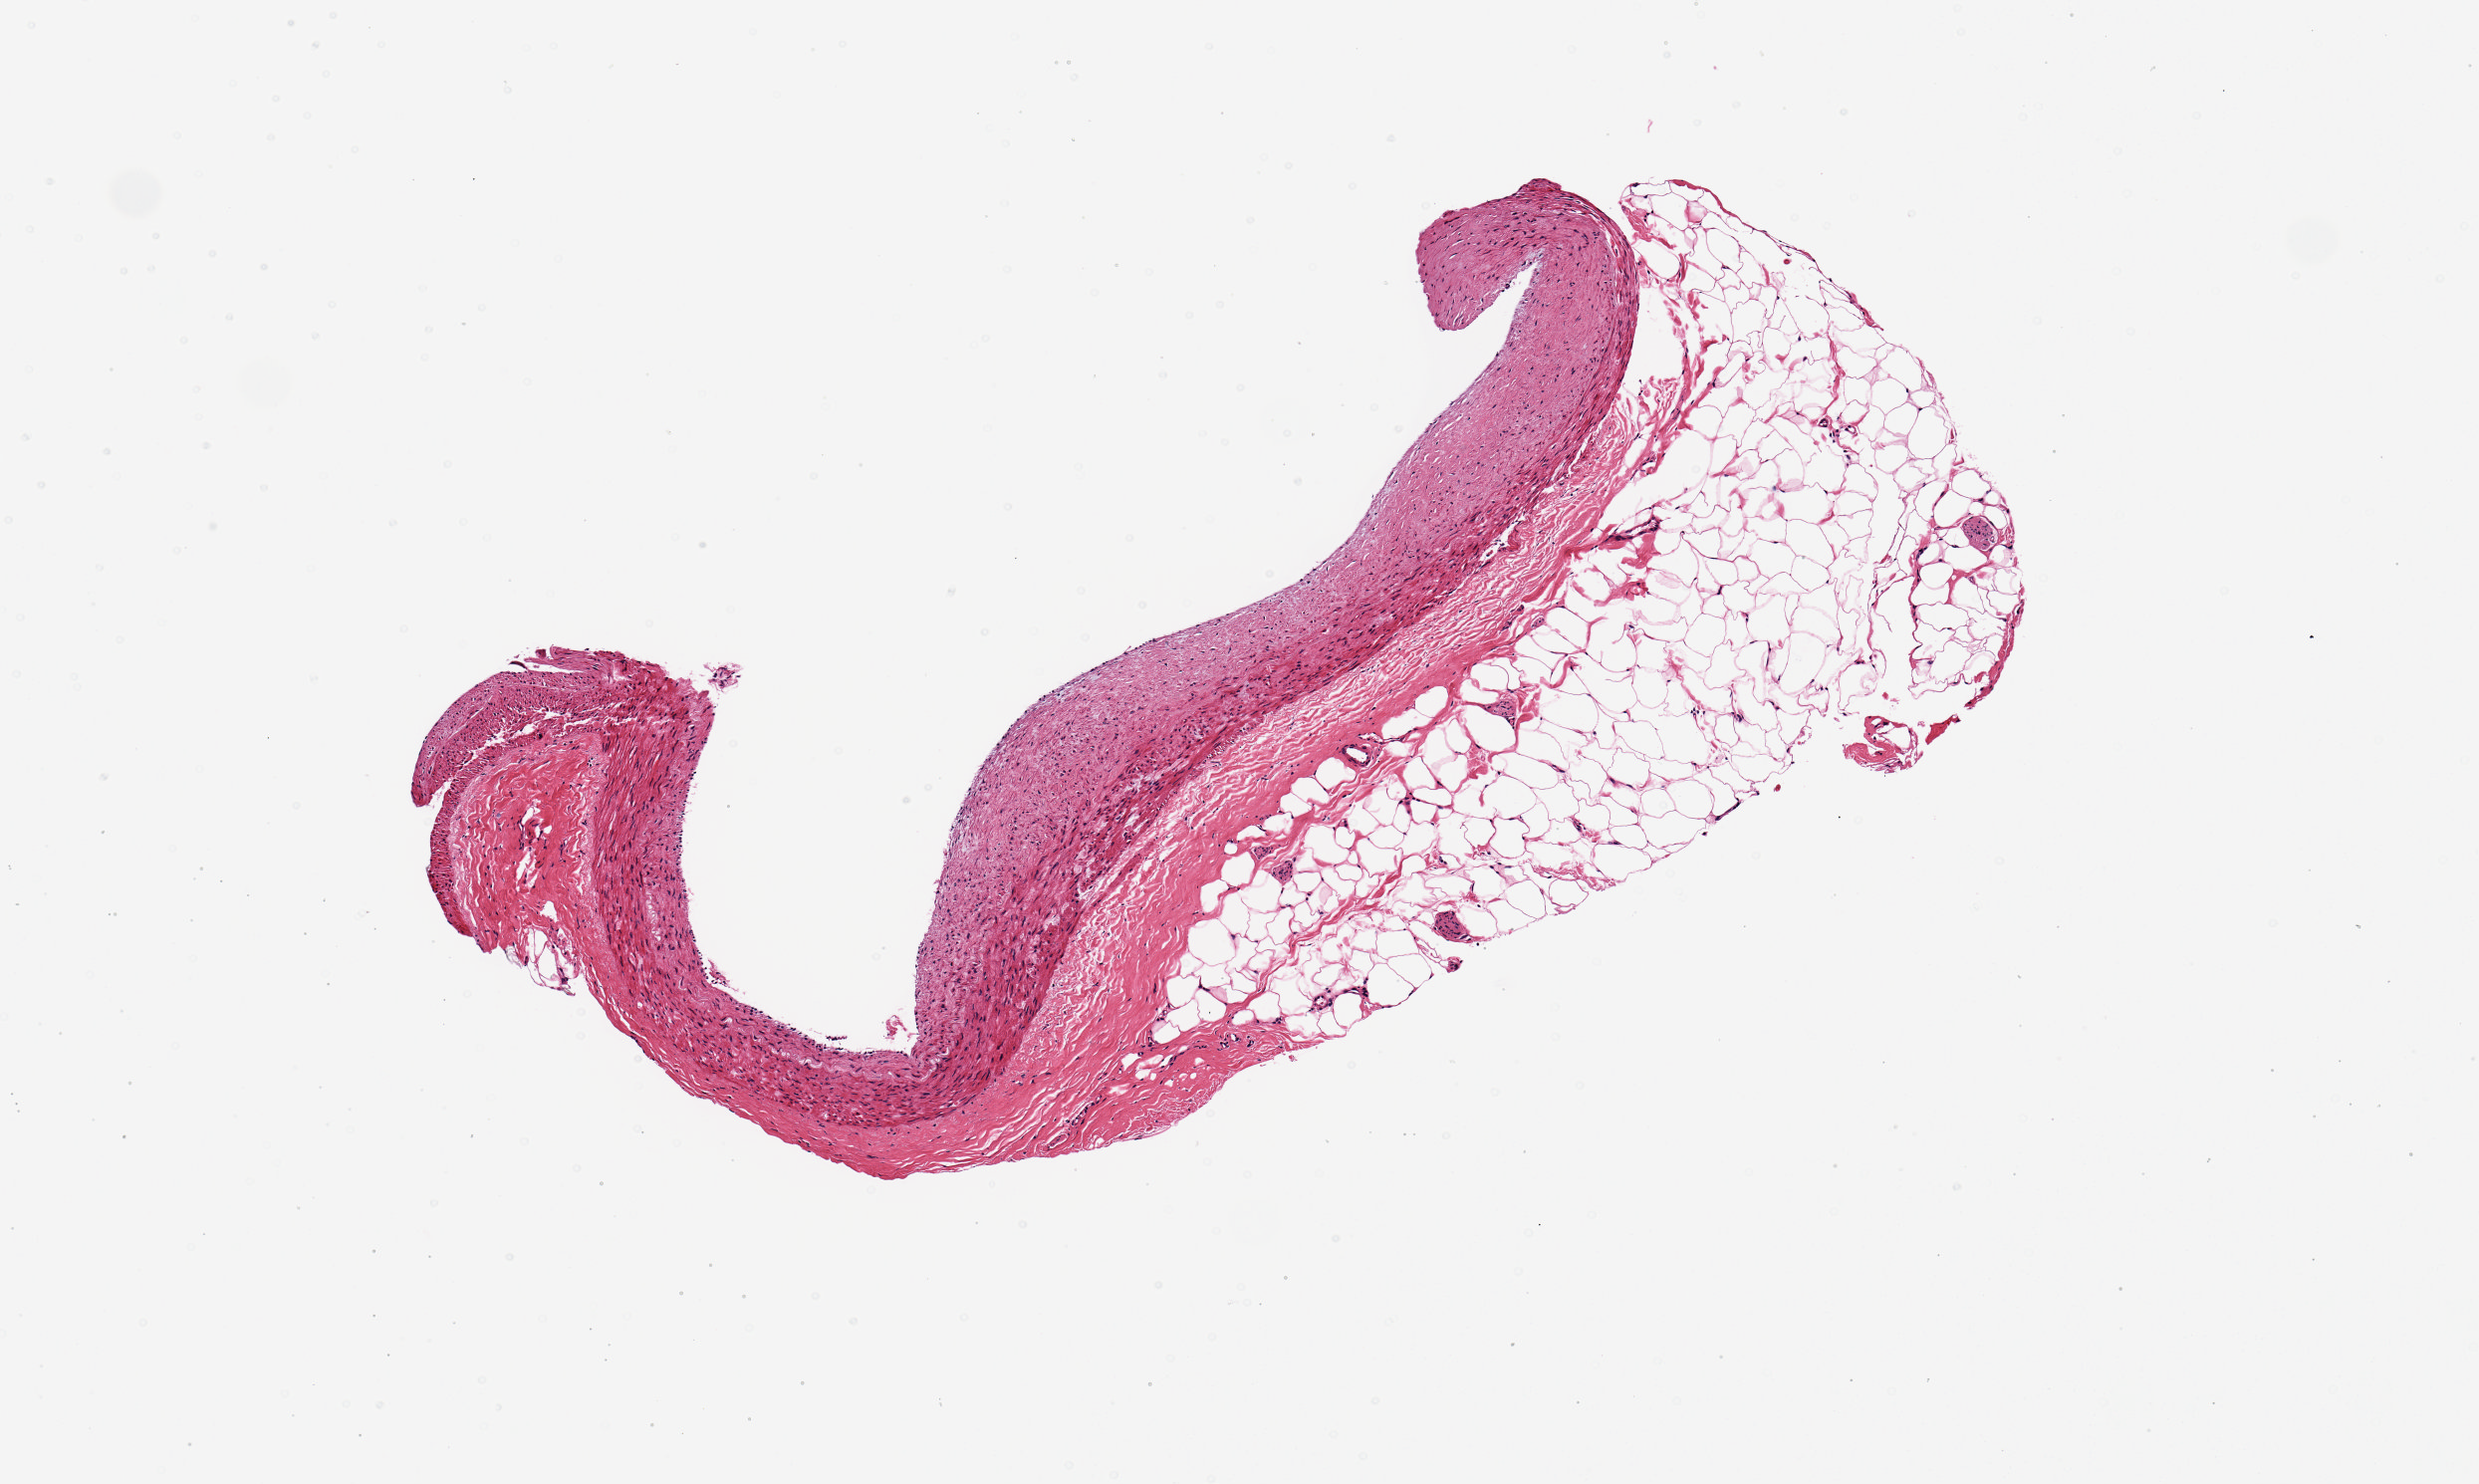
Hematoxylin and eosin (H&E) whole-slide image, shown as a low-resolution overview of the whole scanned area (about 4.9 x 2.9 mm). PAXgene-fixed paraffin-embedded (PFPE) section. Target tissue: coronary artery. Tissue donor sample.
* reviewer comment on this tissue sample: 50% of aliquot is adipose tissue